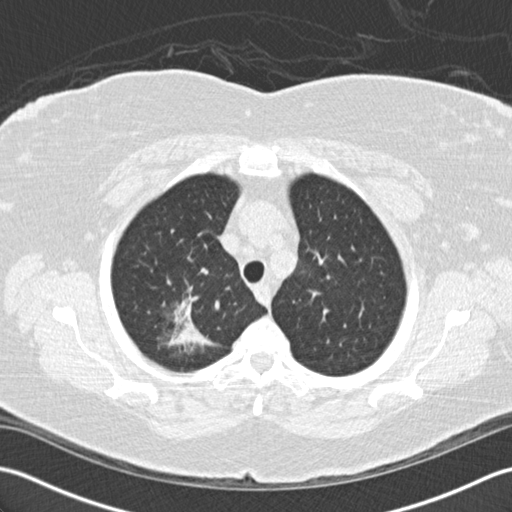
Low-dose screening chest CT, axial slice. First (baseline) screen. Lung window (W 1500 / L -600 HU). 512 × 512 image matrix. Female, age 72 years at enrolment. Former smoker at enrolment.
Lesion marked by an expert reader, bounding box [x1, y1, x2, y2] px = [137, 275, 231, 367]. The screening reader recorded 2 non-calcified nodules or masses ≥4 mm on this exam (right lower lobe, right lower lobe); which of them this box marks is not recorded. Official screen result: positive, change unspecified: nodule(s) >= 4 mm or enlarging nodule(s), mass(es), or other non-specific abnormalities suspicious for lung cancer. Participant outcome: lung cancer diagnosed 494 days after this screen (after the second annual screen) — bronchiolo-alveolar adenocarcinoma, NOS, right upper lobe, stage IIIB (AJCC 6th edition), 45 mm at pathology.